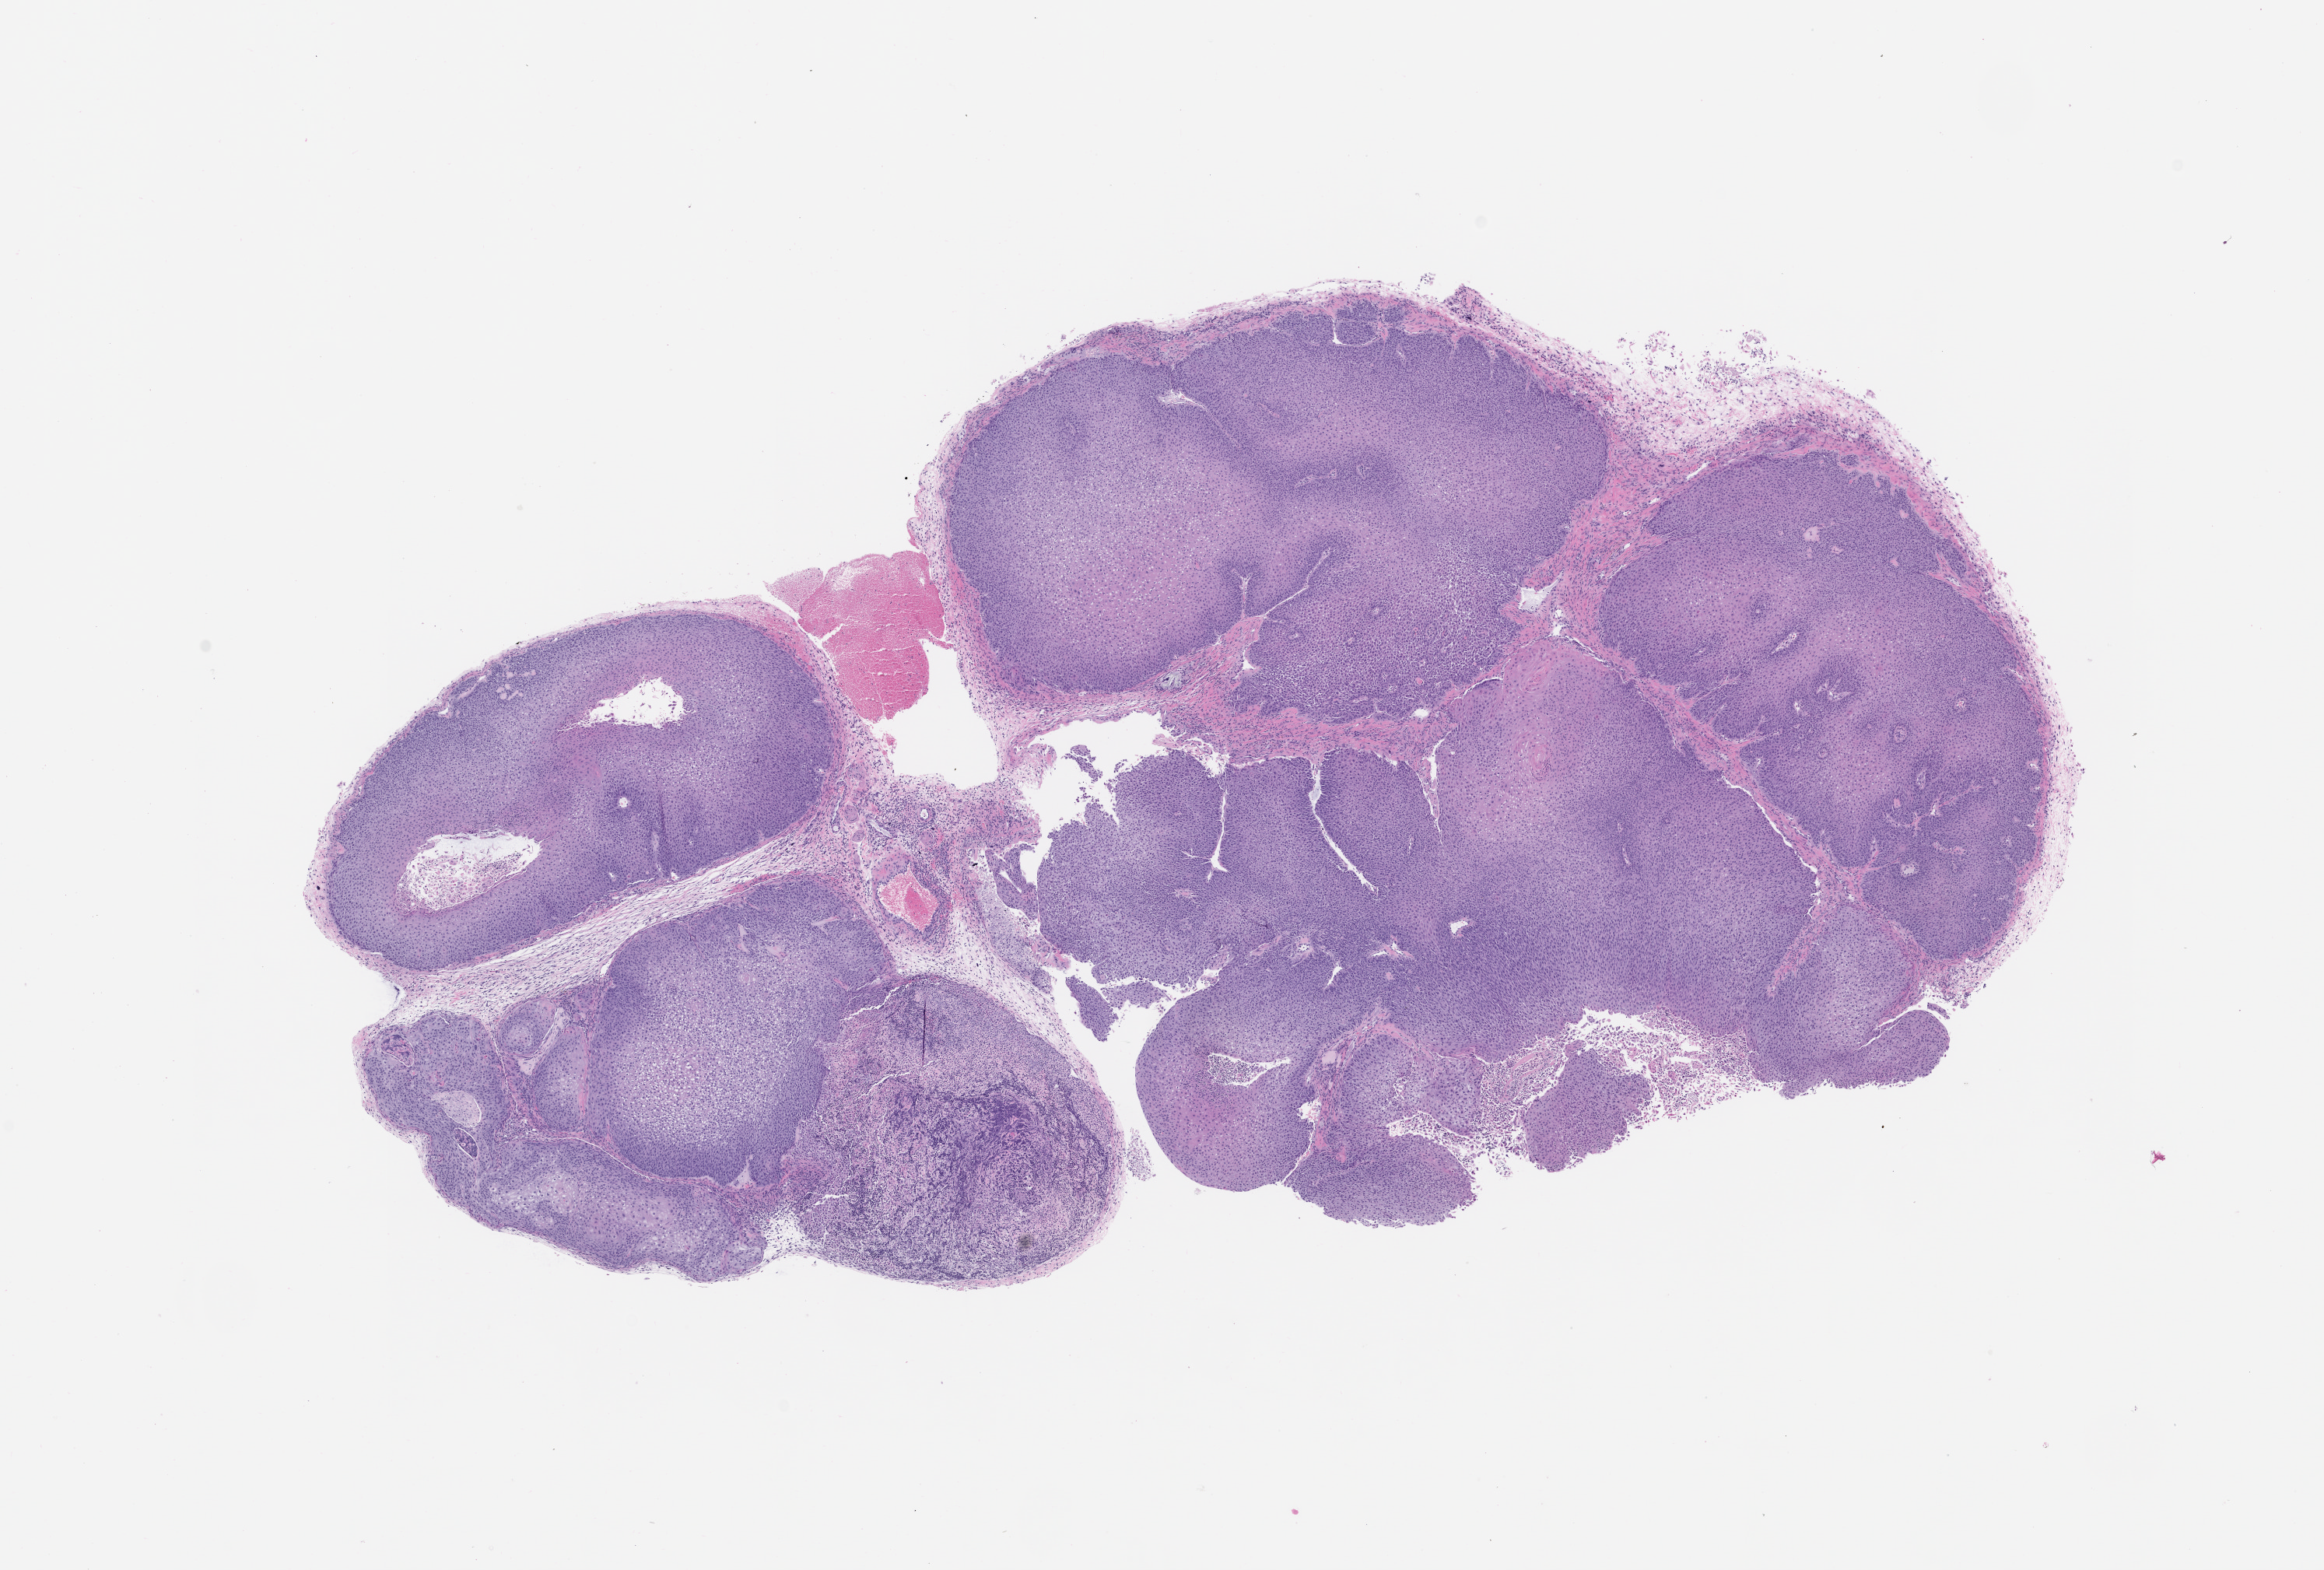
Whole-slide image, H&E: patient-derived xenograft (human tumor grown in a mouse), passage 0 — a low-resolution overview of the entire scanned area, about 12.0 x 8.1 mm. Formalin-fixed, paraffin-embedded (FFPE) tissue. Originating tumor site category: bladder.
* originating patient diagnosis: Transitional Cell Carcinoma